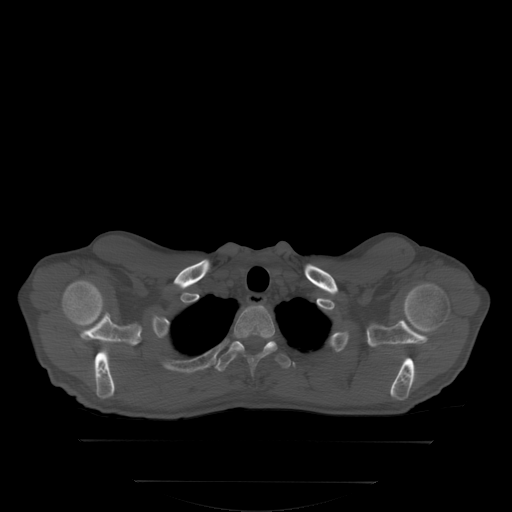
CT including the spine, one axial slice; position 284 of 350 along the scan axis; bone window (W 1800 / L 400 HU); 512 × 512 image matrix, field of view 500 × 500 mm. Male patient, age 58 years. Case-level facts recorded for this patient, not image findings: primary cancer: prostate; vertebrae with lytic lesions (as recorded): L1.
Annotated regions visible in this slice (semi-automatic segmentation, software-assisted and operator-edited):
- T1 vertebra: bounding box <234,307,278,377> (left, top, right, bottom; pixels)
- T2 vertebra: <215,341,290,373>